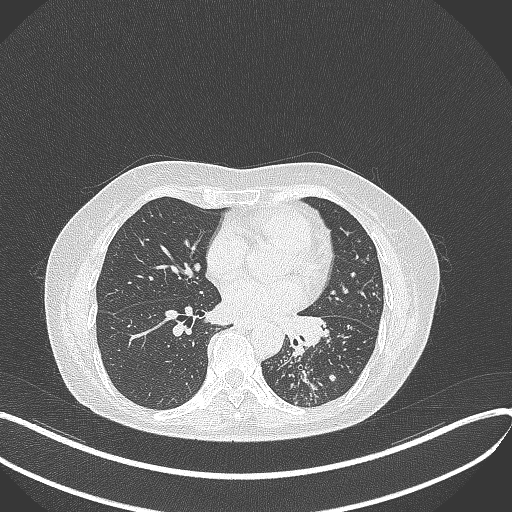
Chest CT, one axial slice; slice 184 of 429 in the series (ordered by position); reconstruction kernel B70f; 100 kVp; lung window (W 1500 / L -600 HU); 1 mm slice thickness; 512 × 512 image matrix. Female patient, age 63 years. From the clinical record (not read from this slice): clinical TNM (as recorded): T1b N0 M0; histopathological grade: G2-3.
Annotated regions visible in this slice (bounding box drawn by a radiologist):
- lung tumour (recorded histology: adenocarcinoma): box from (x=285, y=315) to (x=330, y=353) px